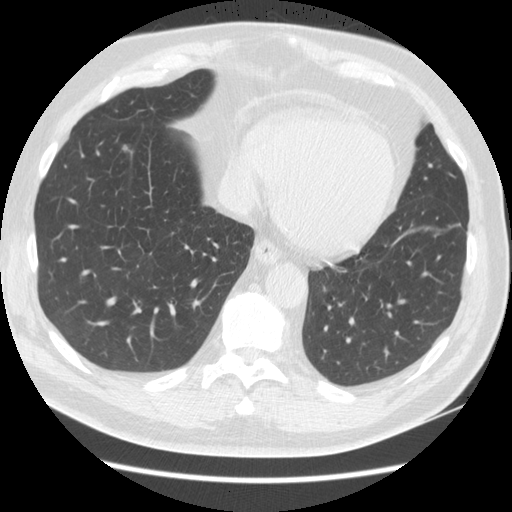
Low-dose screening chest CT, one axial slice. Position 48 of 161 along the scan axis. Reconstruction kernel STANDARD. Lung window (W 1500 / L -600 HU). 512 × 512 image matrix, field of view 360 × 360 mm.
Annotated regions visible in this slice (manually delineated by an expert):
- lesion 1 (tumor, lower lobe of right lung): box from (x=123, y=145) to (x=132, y=154) px